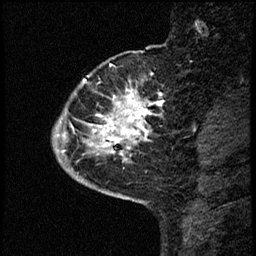
Breast MRI (dynamic contrast-enhanced), one sagittal slice. Slice 12 of 68 in the series (ordered by position). Dynamic contrast-enhanced study with each time point stored as its own series, time point 2 of 3 at this slice position (early post-contrast, ordered by acquisition time). 1.5 T. TE 4.2 ms, TR 17.6 ms. 2 mm slice thickness. 256 × 256 image matrix, field of view 200 × 200 mm. Patient: female, 52 years. Case-level facts recorded for this patient, not image findings: setting: breast cancer imaged before/during neoadjuvant chemotherapy; receptor status: HER2-positive.
Outlined on this slice (semi-automatic segmentation, software-assisted and operator-edited):
- analysis volume of interest (the breast-tissue region the enhancement analysis was run in; not a lesion): bounding box (x1, y1, x2, y2) in pixels: (53, 61, 172, 184)
- tumour enhancement mask (voxels above the 100 % enhancement threshold inside the analysis volume of interest): (57, 90, 160, 181)